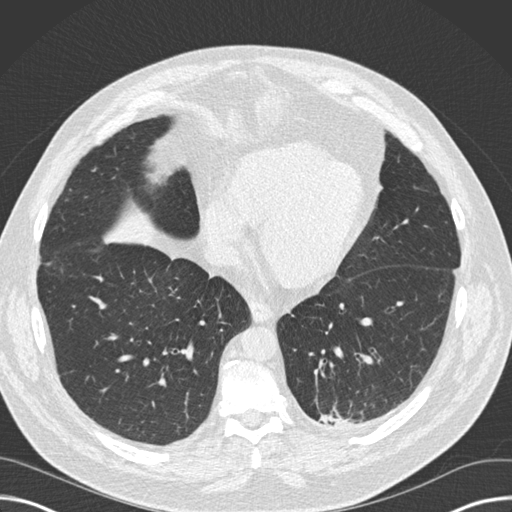
Low-dose screening chest CT, one axial slice. Position 54 of 160 along the scan axis. Reconstruction kernel B30f. Lung window (W 1500 / L -600 HU). 2 mm slice thickness. 512 × 512 image matrix, field of view 382 × 382 mm.
Structures marked on this image (outlined manually by an expert reader):
- lesion 1 (tumor, upper lobe of left lung): bounding box <320,414,350,426> (left, top, right, bottom; pixels)